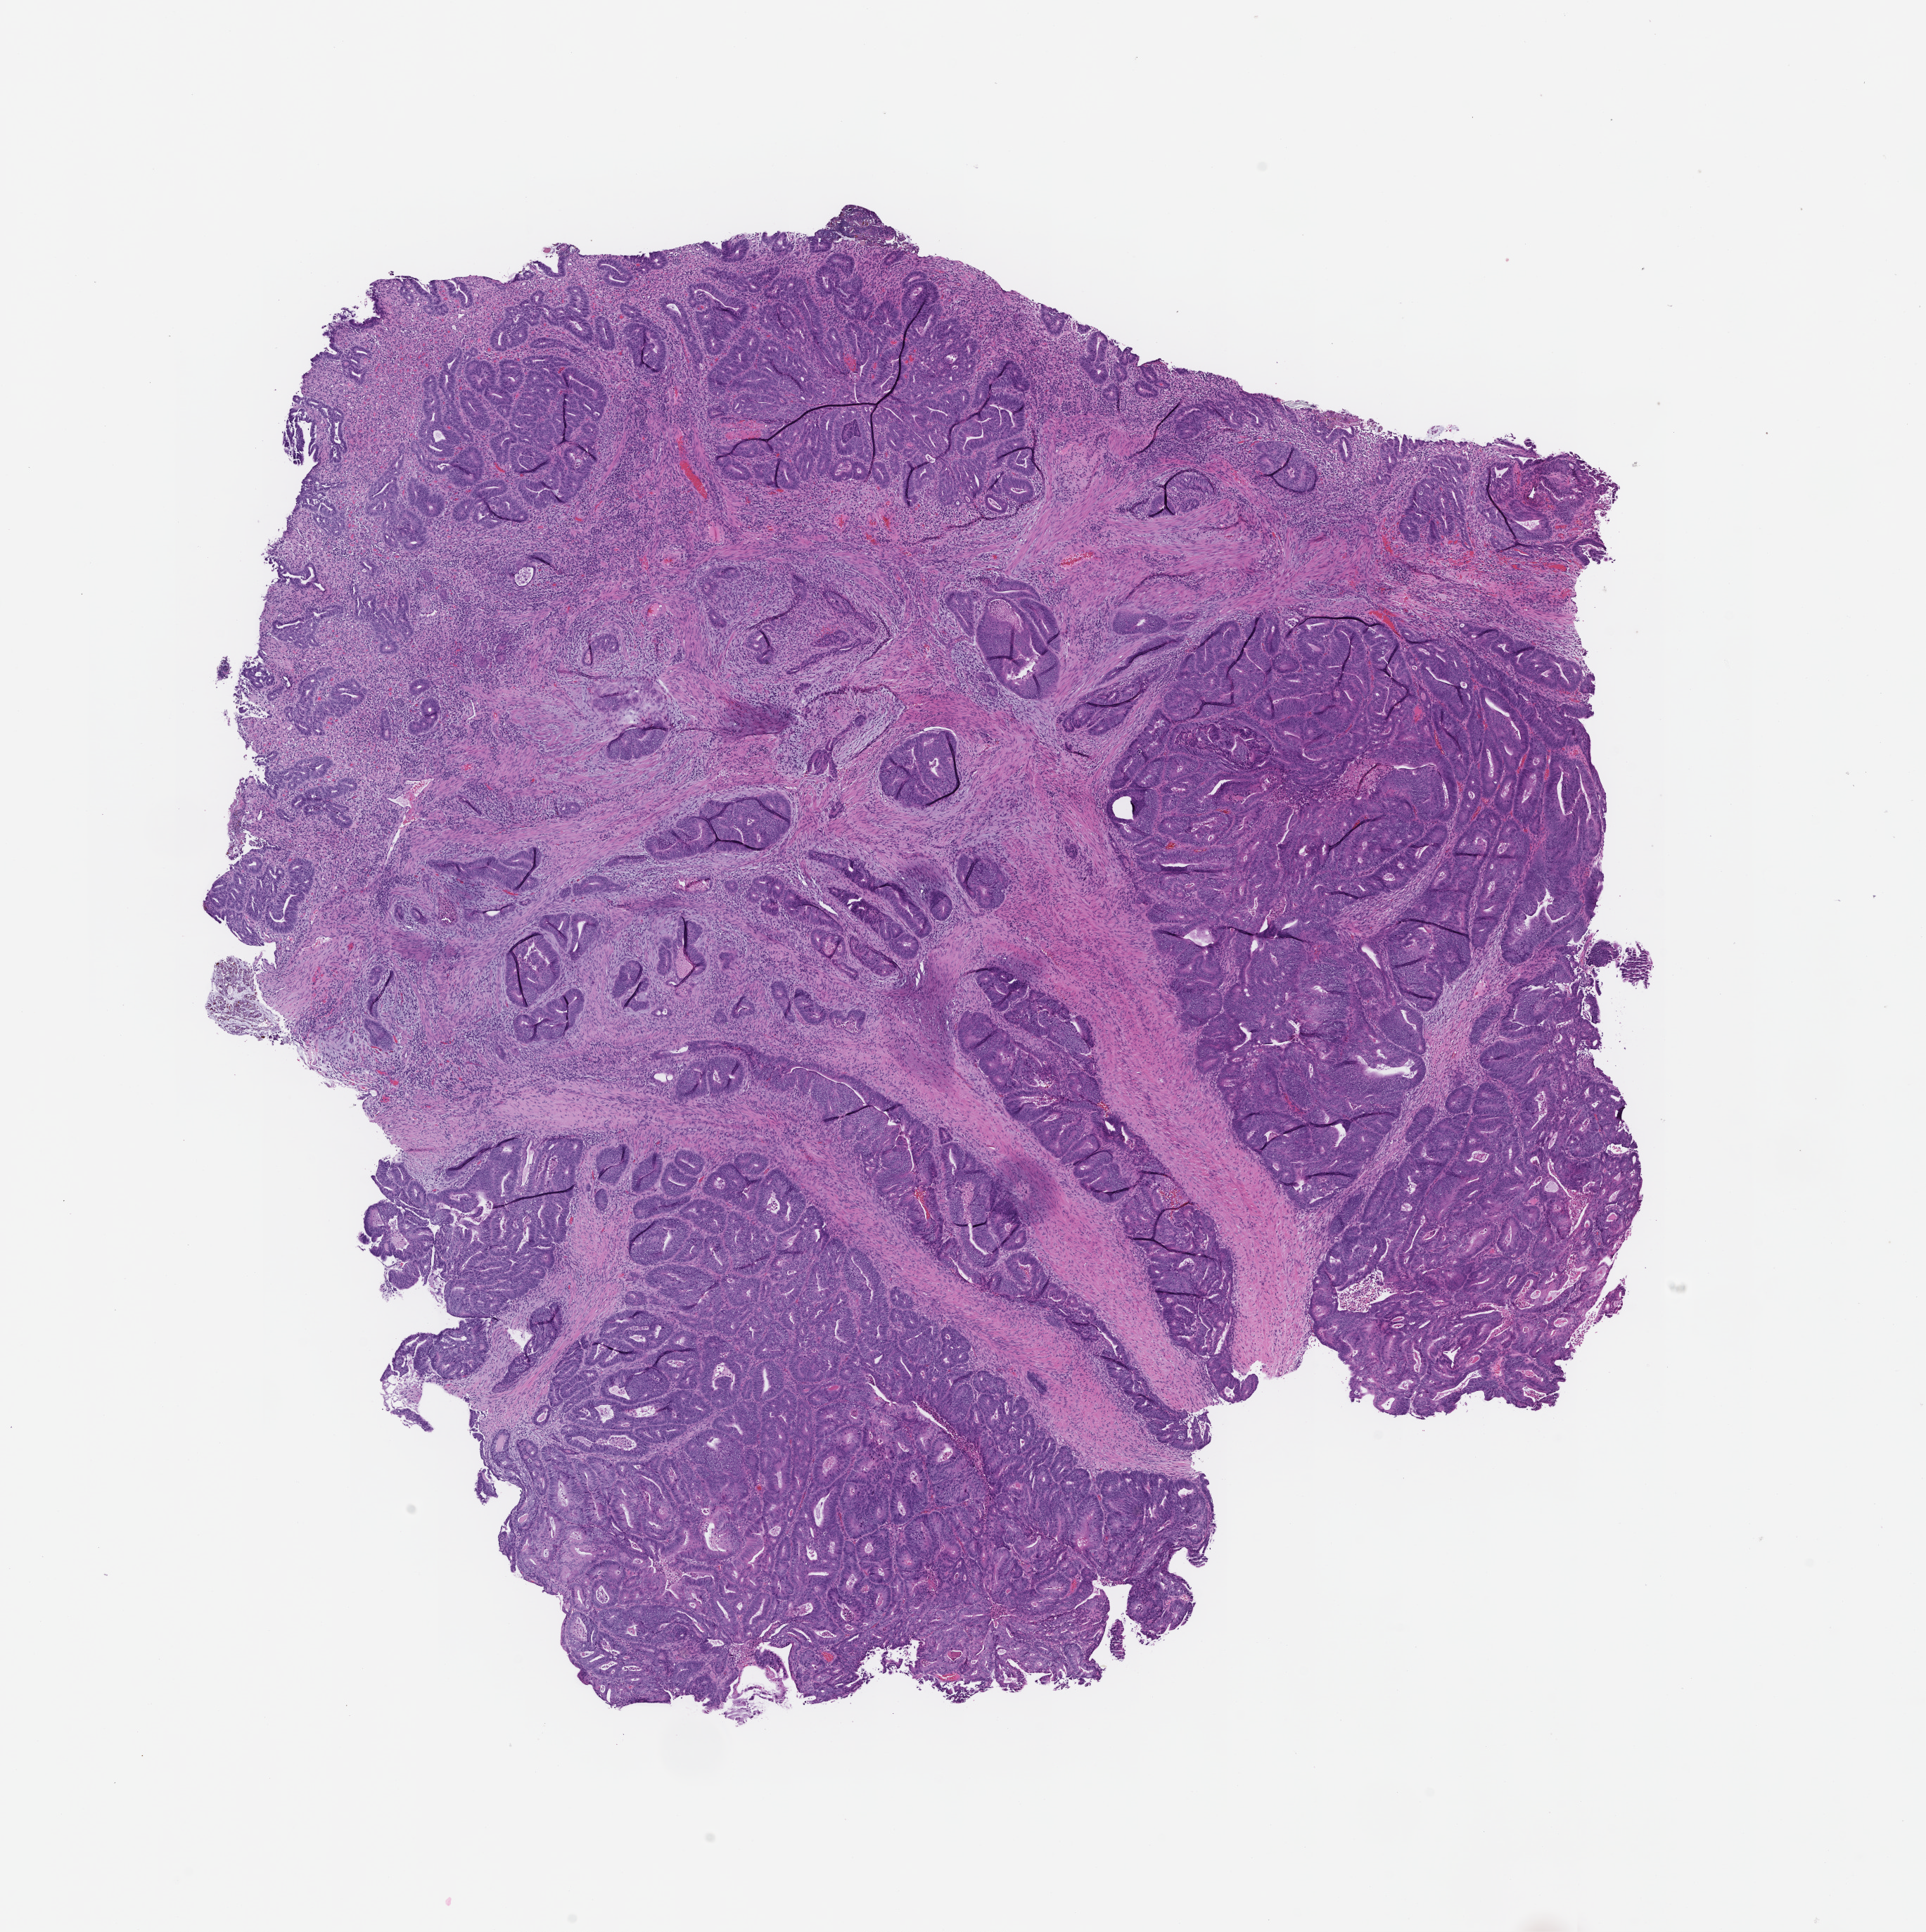
Haematoxylin and eosin whole-slide image, whole scanned area (about 11.1 x 11.1 mm) shown as a low-resolution overview, formalin-fixed, paraffin-embedded (FFPE) tissue, tissue site: colon. Patient: male.
This section: primary tumour tissue. Diagnosis: Colorectal Carcinoma.